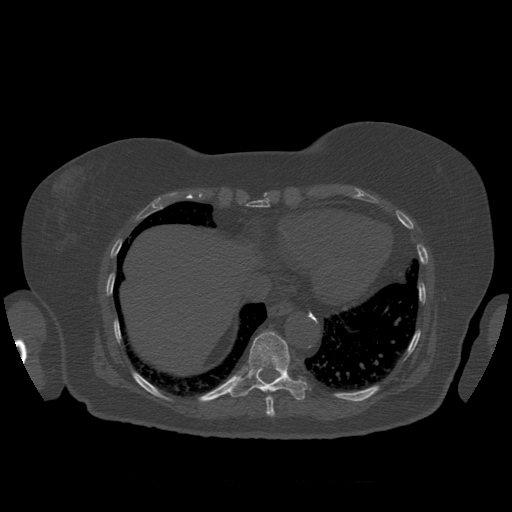
CT including the spine, one axial slice; slice 344 of 399 in the series (ordered by position); reconstruction kernel STANDARD; 120 kVp; bone window (W 1800 / L 400 HU); 1.25 mm slice thickness; 512 × 512 image matrix, field of view 404 × 404 mm. Patient age 81 years. From the clinical record (not read from this slice): primary cancer: renal.
Annotated regions visible in this slice (semi-automatic segmentation, software-assisted and operator-edited):
- T10 vertebra: bounding box (x1, y1, x2, y2) in pixels: (230, 332, 308, 400)
- T9 vertebra: (266, 396, 276, 417)